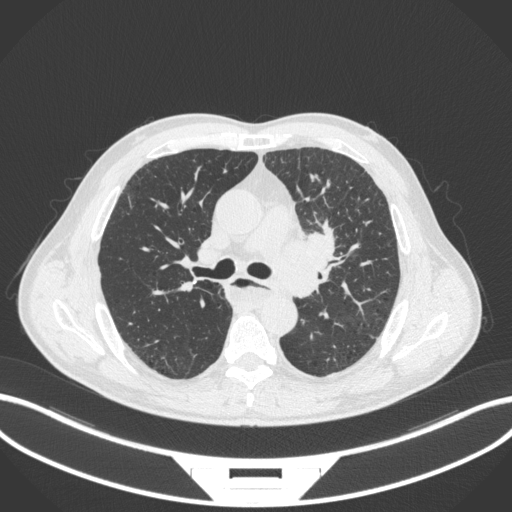
Chest CT, one axial slice; reconstruction kernel B31f; lung window (W 1500 / L -600 HU); 1 mm slice thickness; 512 × 512 image matrix, field of view 400 × 400 mm. Patient: male, 57 years. Case-level facts recorded for this patient, not image findings: clinical TNM (as recorded): T2a N1 M0.
Annotated regions visible in this slice (bounding box drawn by a radiologist):
- lung tumour (recorded histology: squamous cell carcinoma): bounding box <278,220,340,301> (left, top, right, bottom; pixels)